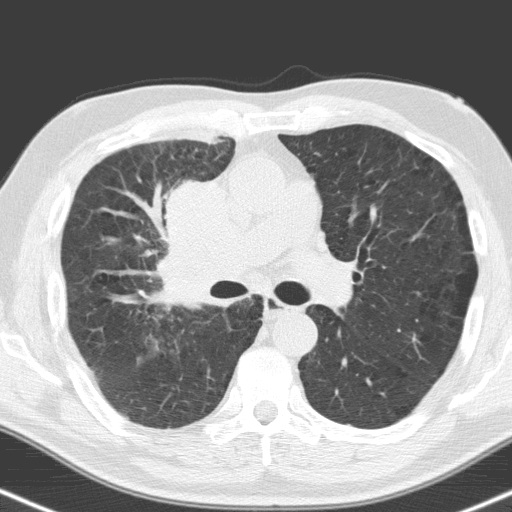
Low-dose screening chest CT, one axial slice; slice 99 of 160 in the series (ordered by position); lung window (W 1500 / L -600 HU); 3.2 mm slice thickness; 512 × 512 image matrix.
Annotated regions visible in this slice (manually delineated by an expert):
- lesion 1 (tumor, hilum of right lung): bounding box [x1, y1, x2, y2] px = [161, 182, 251, 308]